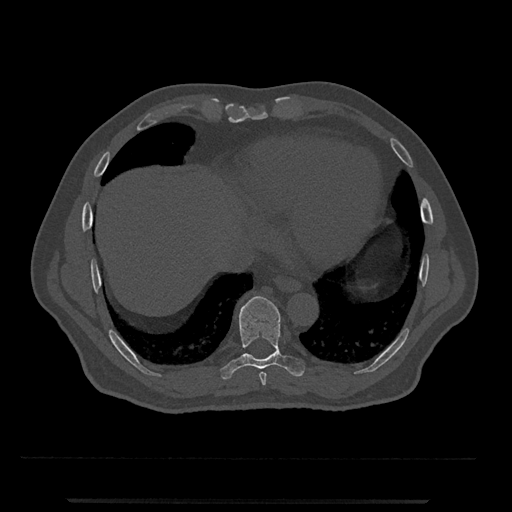
CT including the spine, one axial slice; position 577 of 797 along the scan axis; reconstruction kernel Br40s/3; bone window (W 1800 / L 400 HU); 0.5 mm slice thickness; 512 × 512 image matrix, field of view 419 × 419 mm. Male patient, age 63 years. Case-level facts recorded for this patient, not image findings: primary cancer: prostate.
Structures marked on this image (semi-automatic segmentation, software-assisted and operator-edited):
- T8 vertebra: bounding box <259,372,267,386> (left, top, right, bottom; pixels)
- T9 vertebra: <220,296,305,380>